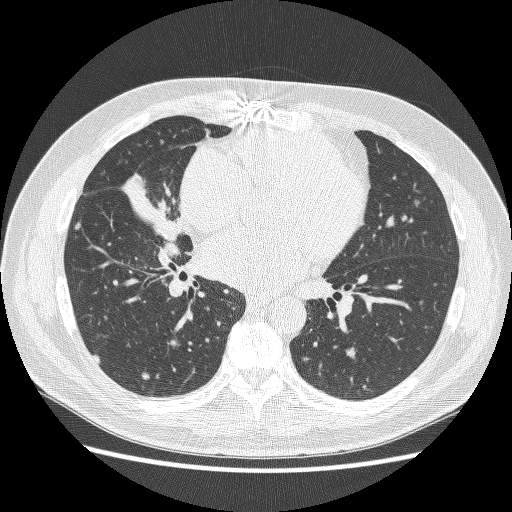
Low-dose screening chest CT, axial slice, first (baseline) screen, lung window (W 1500 / L -600 HU), 1.25 mm slice thickness, slice 126 of 251 in the series, 512 × 512 image matrix. Male participant, aged 59 years at enrolment. Former smoker at enrolment.
Expert reader's lesion annotation, bounding box (x1, y1, x2, y2) in pixels: (112, 164, 196, 249). No non-calcified nodule or mass ≥4 mm was recorded by the screening reader at this exam. Official screen result: positive, change unspecified: nodule(s) >= 4 mm or enlarging nodule(s), mass(es), or other non-specific abnormalities suspicious for lung cancer. Later outcome: lung cancer diagnosed 24 days after this screen — adenocarcinoma, NOS, right middle lobe, poorly differentiated (G3), stage IV (AJCC 6th edition), 54 mm at pathology.